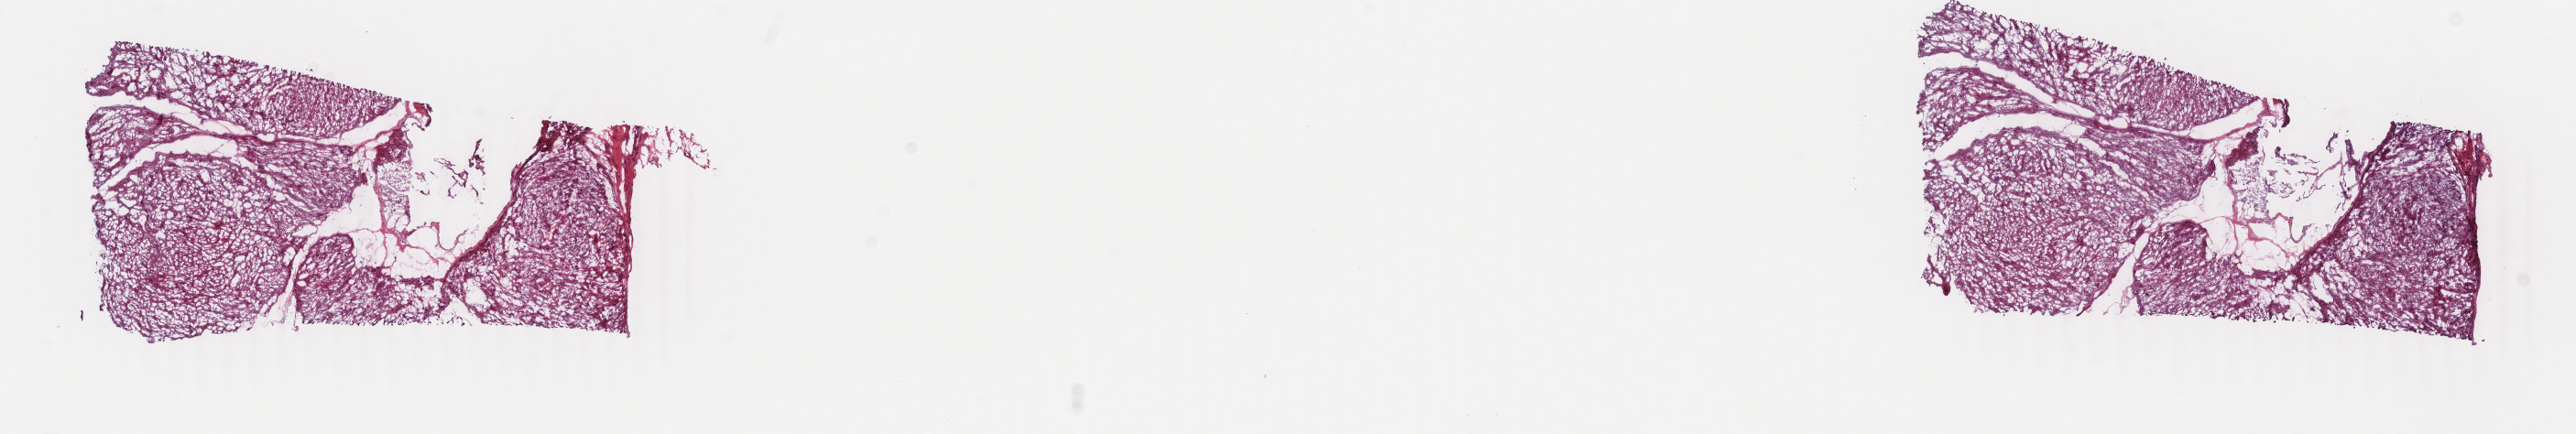
Whole-slide histology image, H&E, low-resolution overview of the scanned area, about 22.4 x 3.8 mm (from a 40x scan), frozen section from the top of the tissue portion, retroperitoneum and peritoneum, primary tumour sample. Patient: male, age at initial diagnosis 74 years. Pathologist review of this section (percent, as recorded): tumour cells 95%, tumour nuclei 95%, normal cells 0%, stromal cells 5%, necrosis 0%. Inflammatory infiltration, as recorded: lymphocyte infiltration 0%, monocyte infiltration 0%, neutrophil infiltration 0%.
Histologic diagnosis: Leiomyosarcoma, NOS (retroperitoneum).